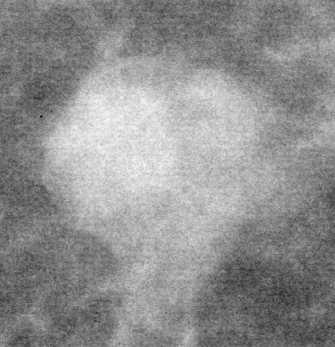
Region of interest cut from a scanned film mammogram (one marked finding); left breast; CC view; BI-RADS breast density category 1 (scale 1–4).
Mass, shape oval, margins spiculated; BI-RADS assessment category 5; pathology (as recorded): malignant.